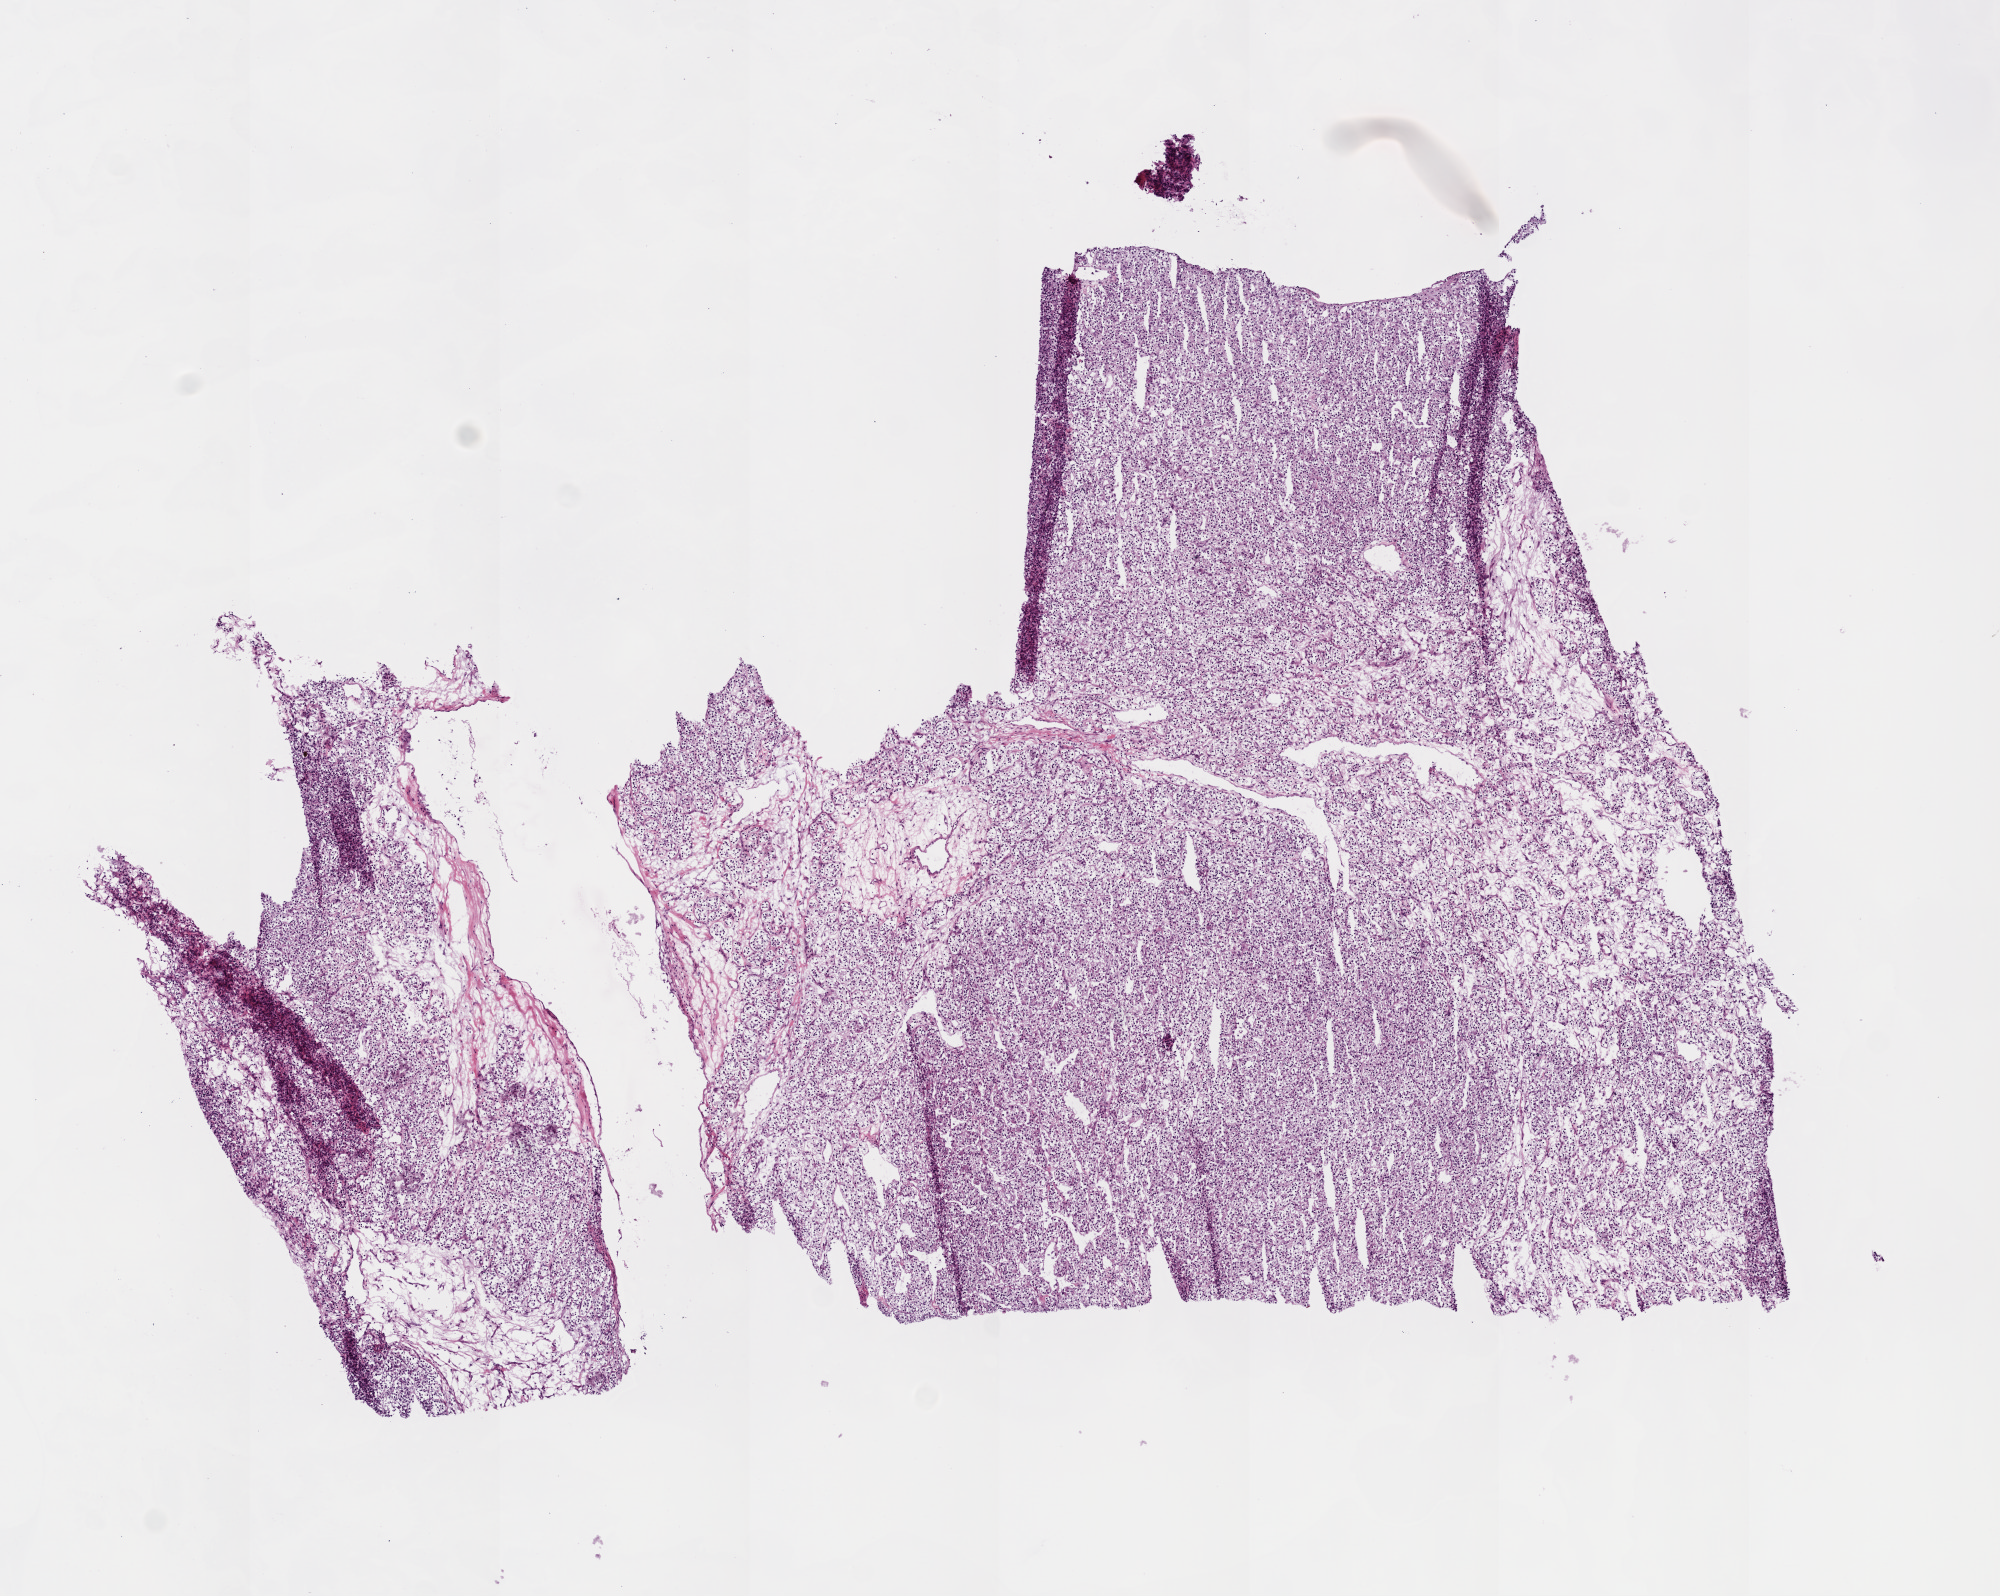
Digitized Hematoxylin and eosin (H&E) stained tissue section (whole slide), low-resolution overview of the scanned area, about 8.0 x 6.4 mm, frozen section from the top of the tissue portion, sample: primary tumour, kidney. Patient: male, age at initial diagnosis 51 years. Histologic grade: G2 (moderately differentiated). Composition of this section per pathologist review: tumour cells 85%, tumour nuclei 85%, normal cells 0%, stromal cells 15%, necrosis 0%.
* AJCC pathologic stage: IV
* TNM: T3b N0 M1
* laterality: right
* diagnosis: Clear cell adenocarcinoma, NOS